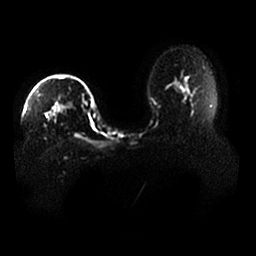
Breast MRI, one axial slice. Diffusion-weighted series; image 2 of 4 stored at this slice position (different b-values; order by instance number). 1.5 T. 256 × 256 image matrix, field of view 400 × 400 mm. Female patient.
Outlined on this slice (outlined manually by an expert reader):
- tumour on diffusion-weighted imaging: box from (x=54, y=98) to (x=72, y=113) px